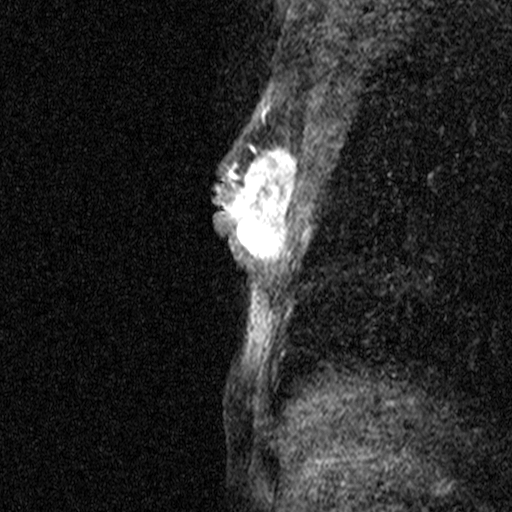
Breast MRI (dynamic contrast-enhanced), one sagittal slice. Position 27 of 44 along the scan axis. Dynamic contrast-enhanced study with each time point stored as its own series, time point 2 of 3 at this slice position (early post-contrast, ordered by acquisition time). 1.5 T. TE 4.5 ms, TR 11 ms. 3 mm slice thickness. 512 × 512 image matrix. Female patient, age 44 years. From the clinical record (not read from this slice): setting: breast cancer imaged before/during neoadjuvant chemotherapy; receptor status: HR-positive, HER2-negative.
Structures marked on this image (semi-automatically segmented with operator editing):
- analysis volume of interest (the breast-tissue region the enhancement analysis was run in; not a lesion): bounding box (x1, y1, x2, y2) in pixels: (218, 118, 293, 291)
- tumour enhancement mask (voxels above the 90 % enhancement threshold inside the analysis volume of interest): (226, 130, 293, 256)